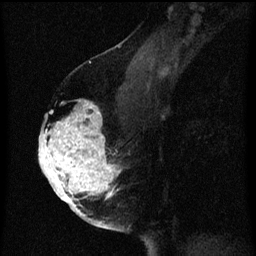
Breast MRI (dynamic contrast-enhanced), one sagittal slice; slice 38 of 60 in the series (ordered by position); dynamic contrast-enhanced series, image 2 of 3 at this slice position (ordered by acquisition); 1.5 T; TE 4.2 ms, TR 8 ms; 2 mm slice thickness; 256 × 256 image matrix. Female patient, age 56 years.
Outlined on this slice (semi-automatic segmentation, software-assisted and operator-edited):
- analysis volume of interest (the breast-tissue region the enhancement analysis was run in; not a lesion): bounding box [x1, y1, x2, y2] px = [40, 104, 125, 219]
- tumour enhancement mask (voxels above the 70 % enhancement threshold inside the analysis volume of interest): [40, 104, 121, 219]